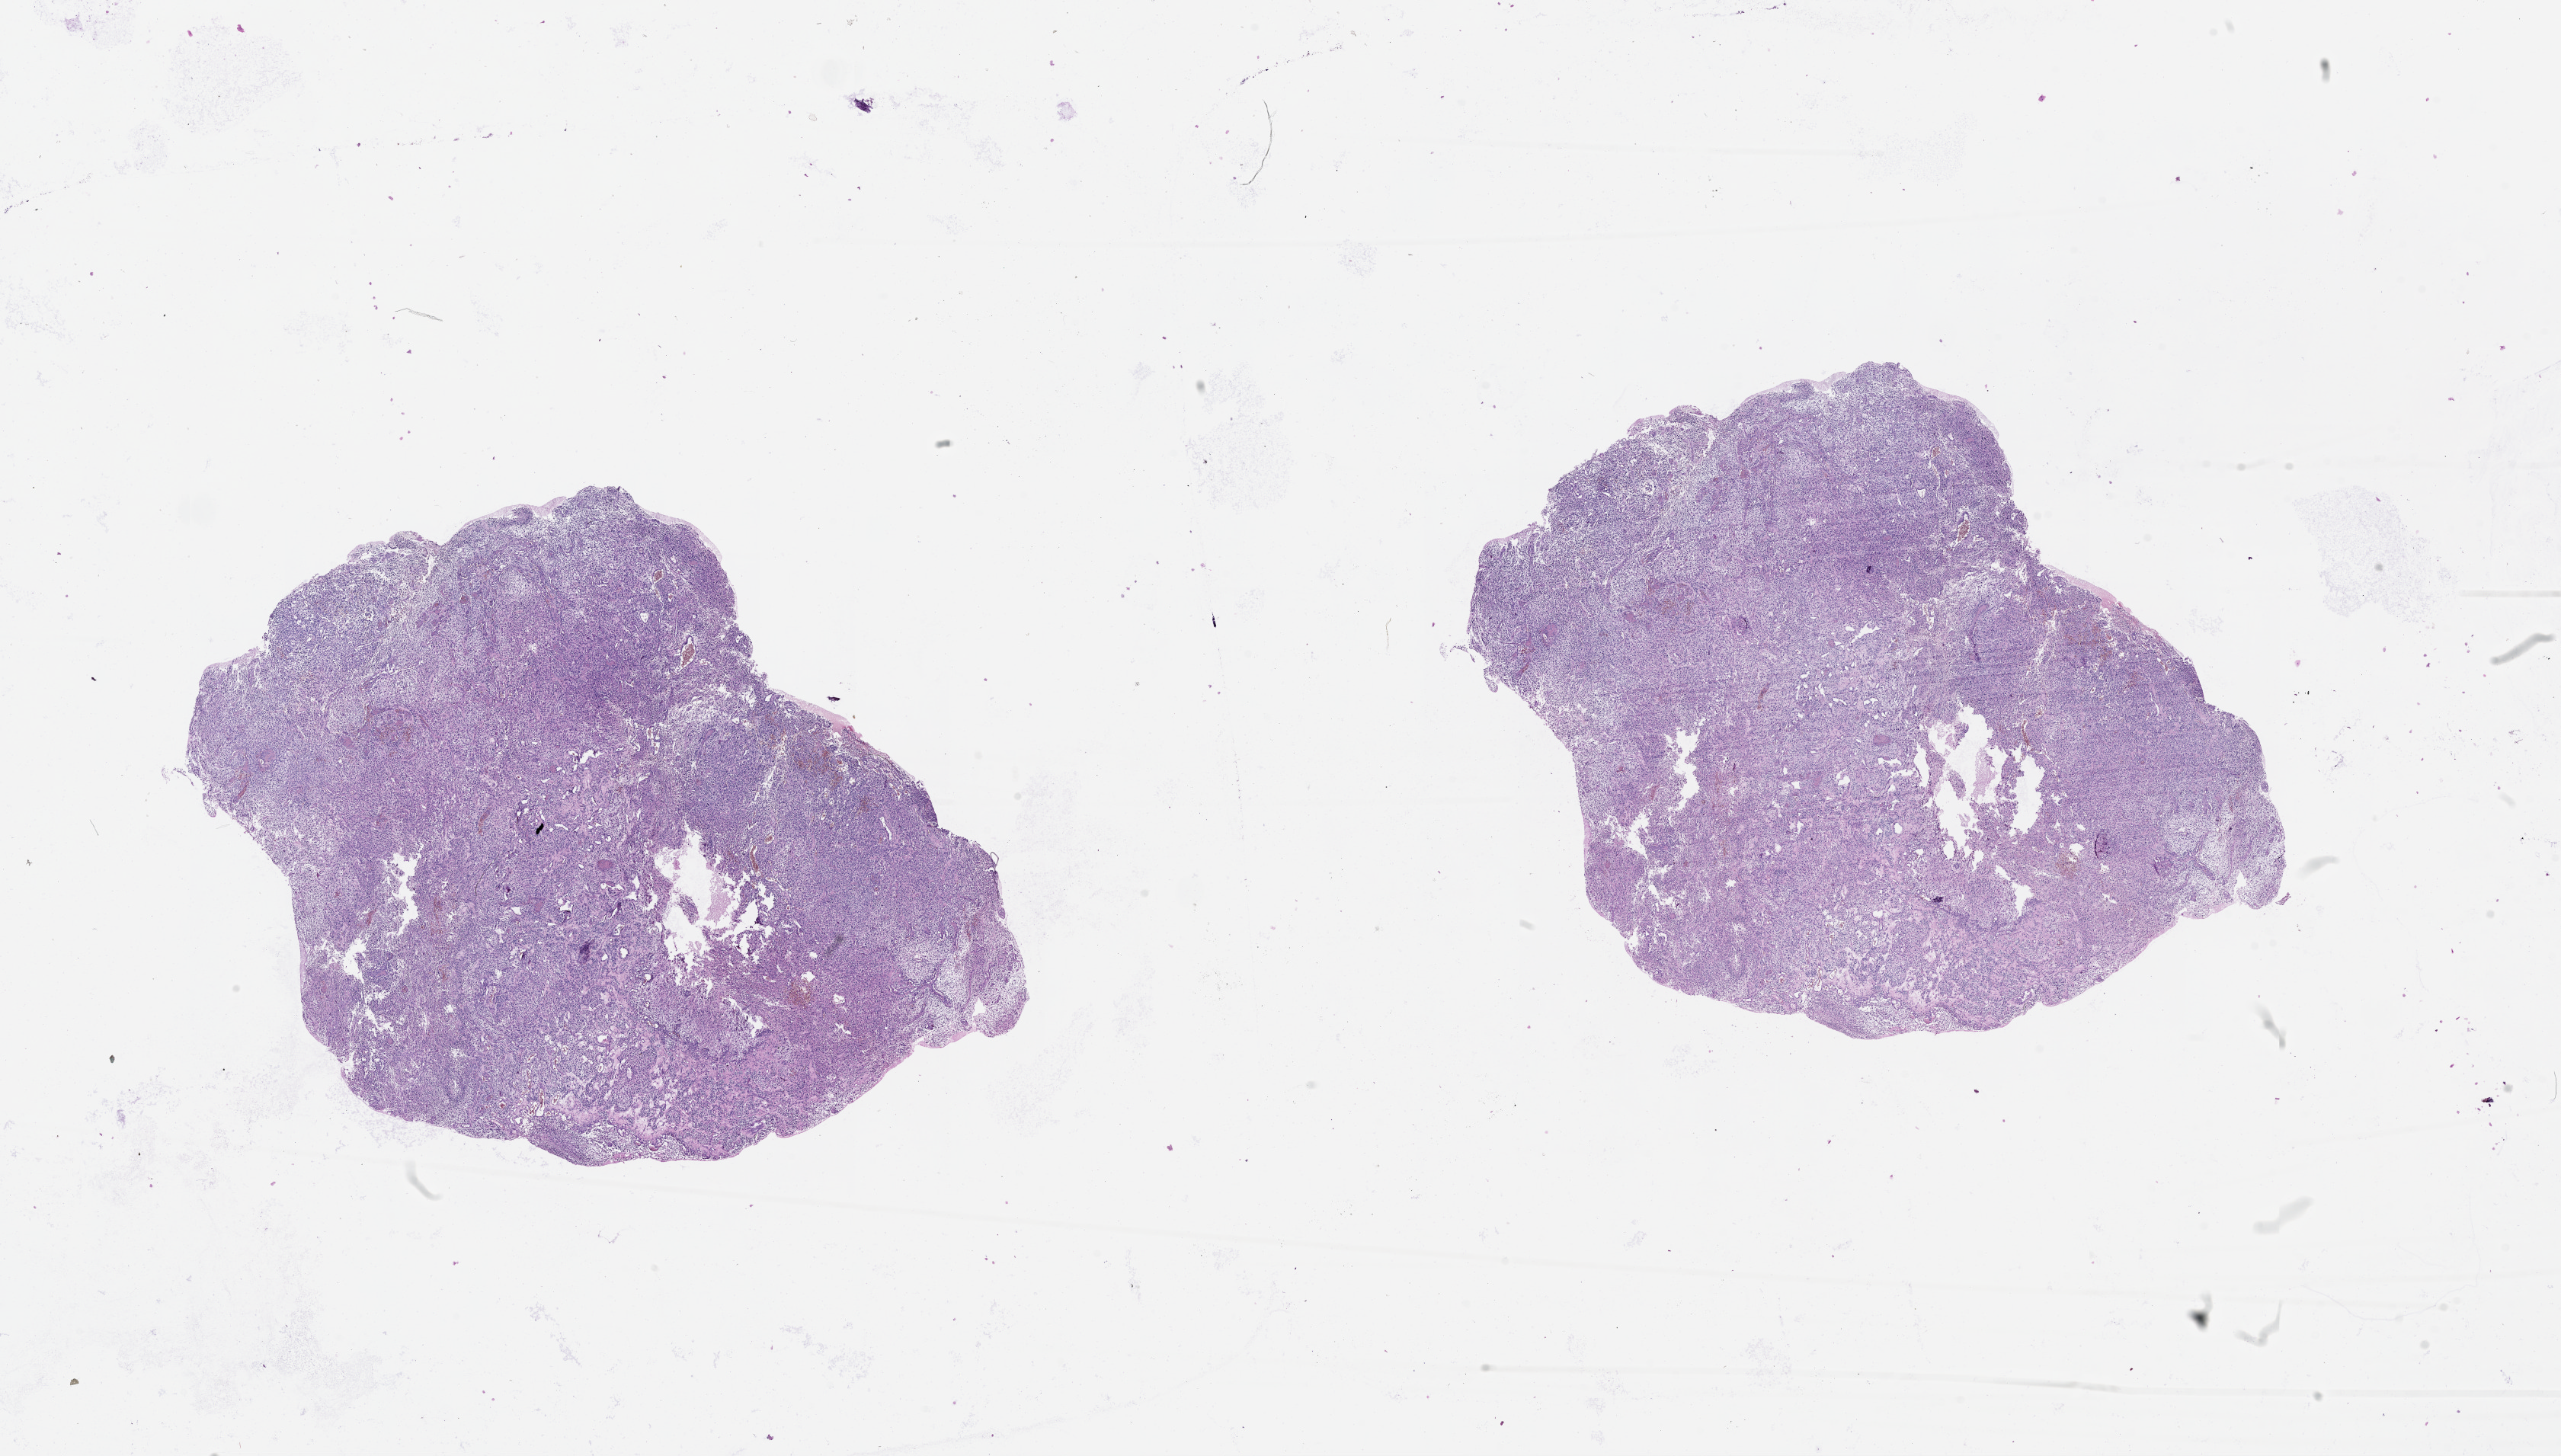
Digitized H&E-stained tissue section (whole slide), low-resolution overview of the scanned area, about 27.1 x 15.4 mm; tumour tissue sample, sampled site: brain. Patient: male, age 65 years. Composition of this section per pathologist review: tumour nuclei 80%, necrosis 10%.
- diagnosis: Glioblastoma
- primary tumour site (as recorded): parietal lobe